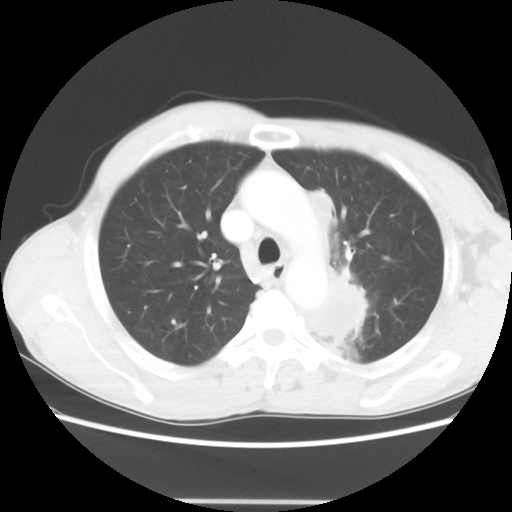
Chest CT, one axial slice. Position 47 of 62 along the scan axis. Reconstruction kernel STANDARD. 100 kVp. Lung window (W 1500 / L -600 HU). 5 mm slice thickness. 512 × 512 image matrix, field of view 360 × 360 mm. Patient: male, 61 years. Case-level facts recorded for this patient, not image findings: clinical TNM (as recorded): T3 N1 M1.
Annotated regions visible in this slice (rectangle marked by the reading radiologist):
- lung tumour (recorded histology: adenocarcinoma): box from (x=304, y=265) to (x=375, y=360) px
- lung tumour (recorded histology: adenocarcinoma): (x=306, y=186)–(x=336, y=260)